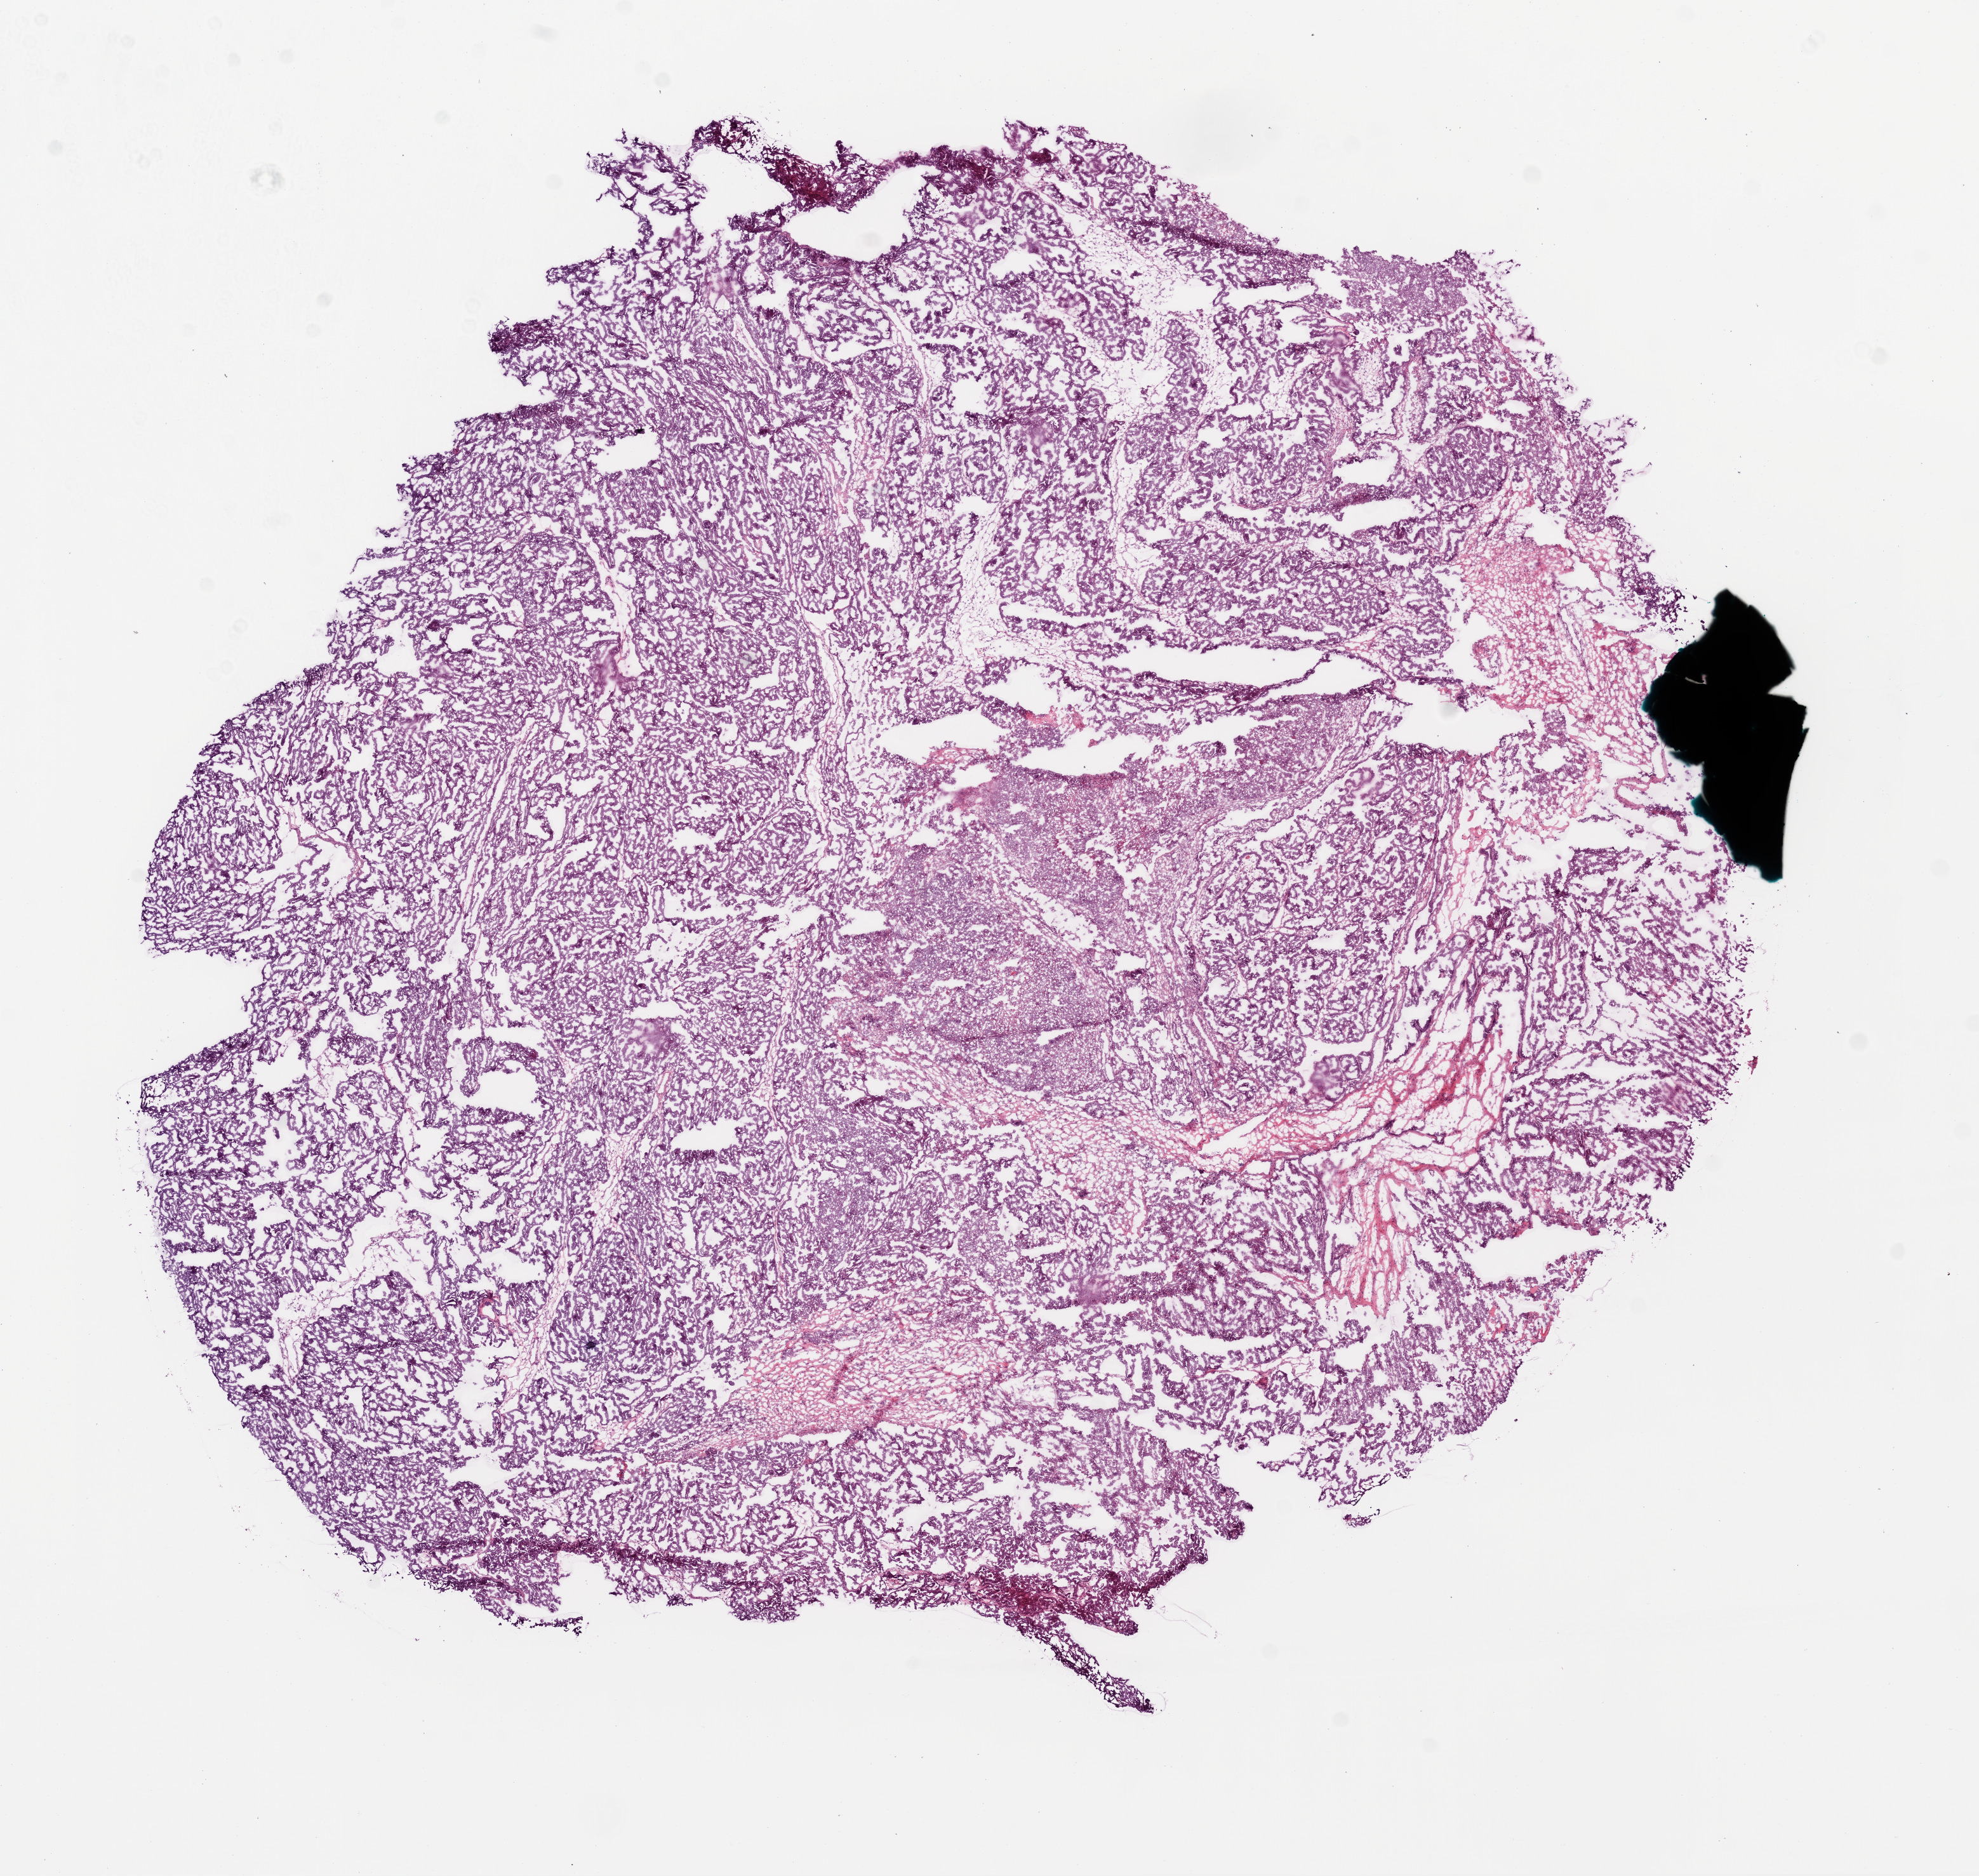
Digitized H&E tissue section (whole slide) — shown as a low-resolution overview of the whole scanned area (about 12.6 x 11.9 mm). Frozen section from the bottom of the tissue portion. Sample: primary tumour, ovary. Patient: female, age at initial diagnosis 78 years.
Diagnosis: Serous cystadenocarcinoma, NOS.